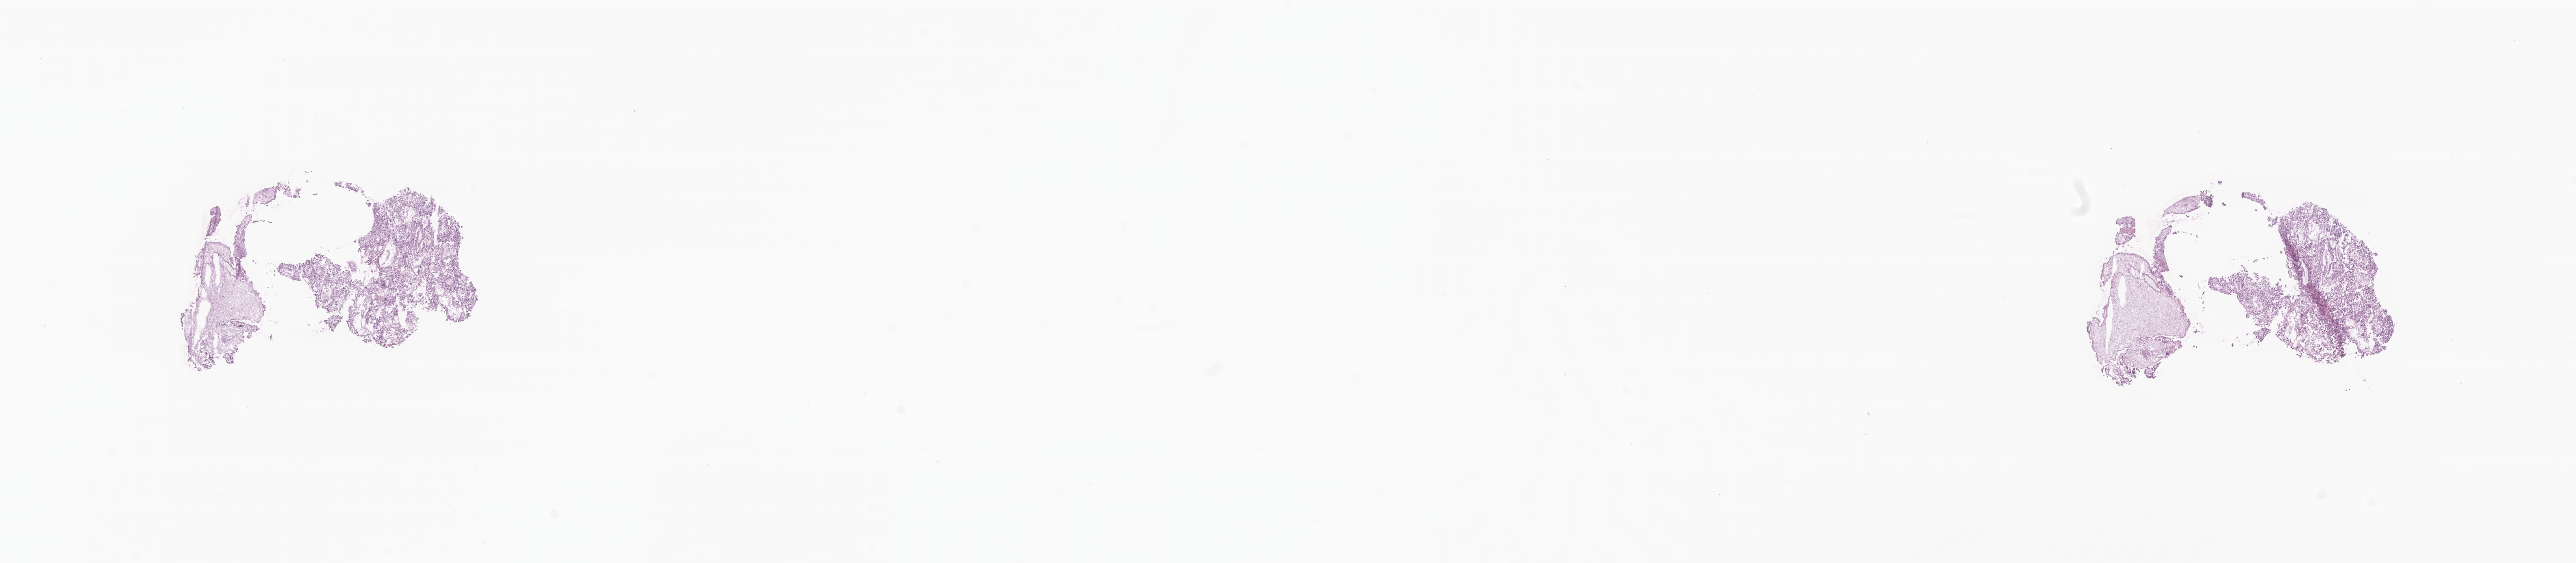
Whole-slide image, haematoxylin and eosin stain of tumor tissue from the cauda equina — whole scanned area (about 26.7 x 5.8 mm) shown as a low-resolution overview, cryosection (OCT / tissue freezing medium). Patient: male, age 143 months (11 years 11 months).
Recorded diagnosis: Myxopapillary ependymoma.